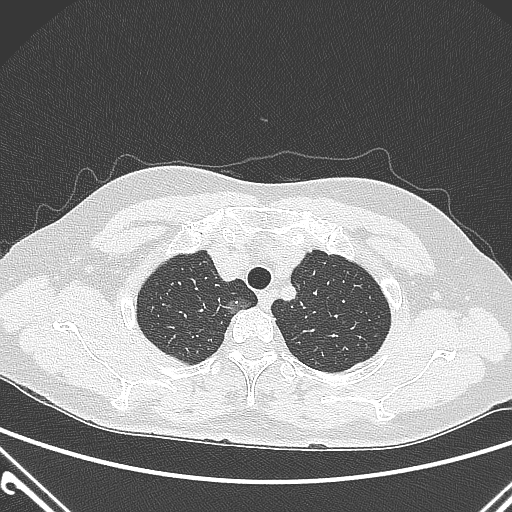
Chest CT, one axial slice; position 242 of 300 along the scan axis; lung window (W 1500 / L -600 HU); 1 mm slice thickness; 512 × 512 image matrix. Female patient, age 54 years. From the clinical record (not read from this slice): clinical TNM (as recorded): T1a N0 M0; histopathological grade: G1.
Annotated regions visible in this slice (rectangle marked by the reading radiologist):
- lung tumour (recorded histology: adenocarcinoma): box from (x=222, y=291) to (x=263, y=324) px